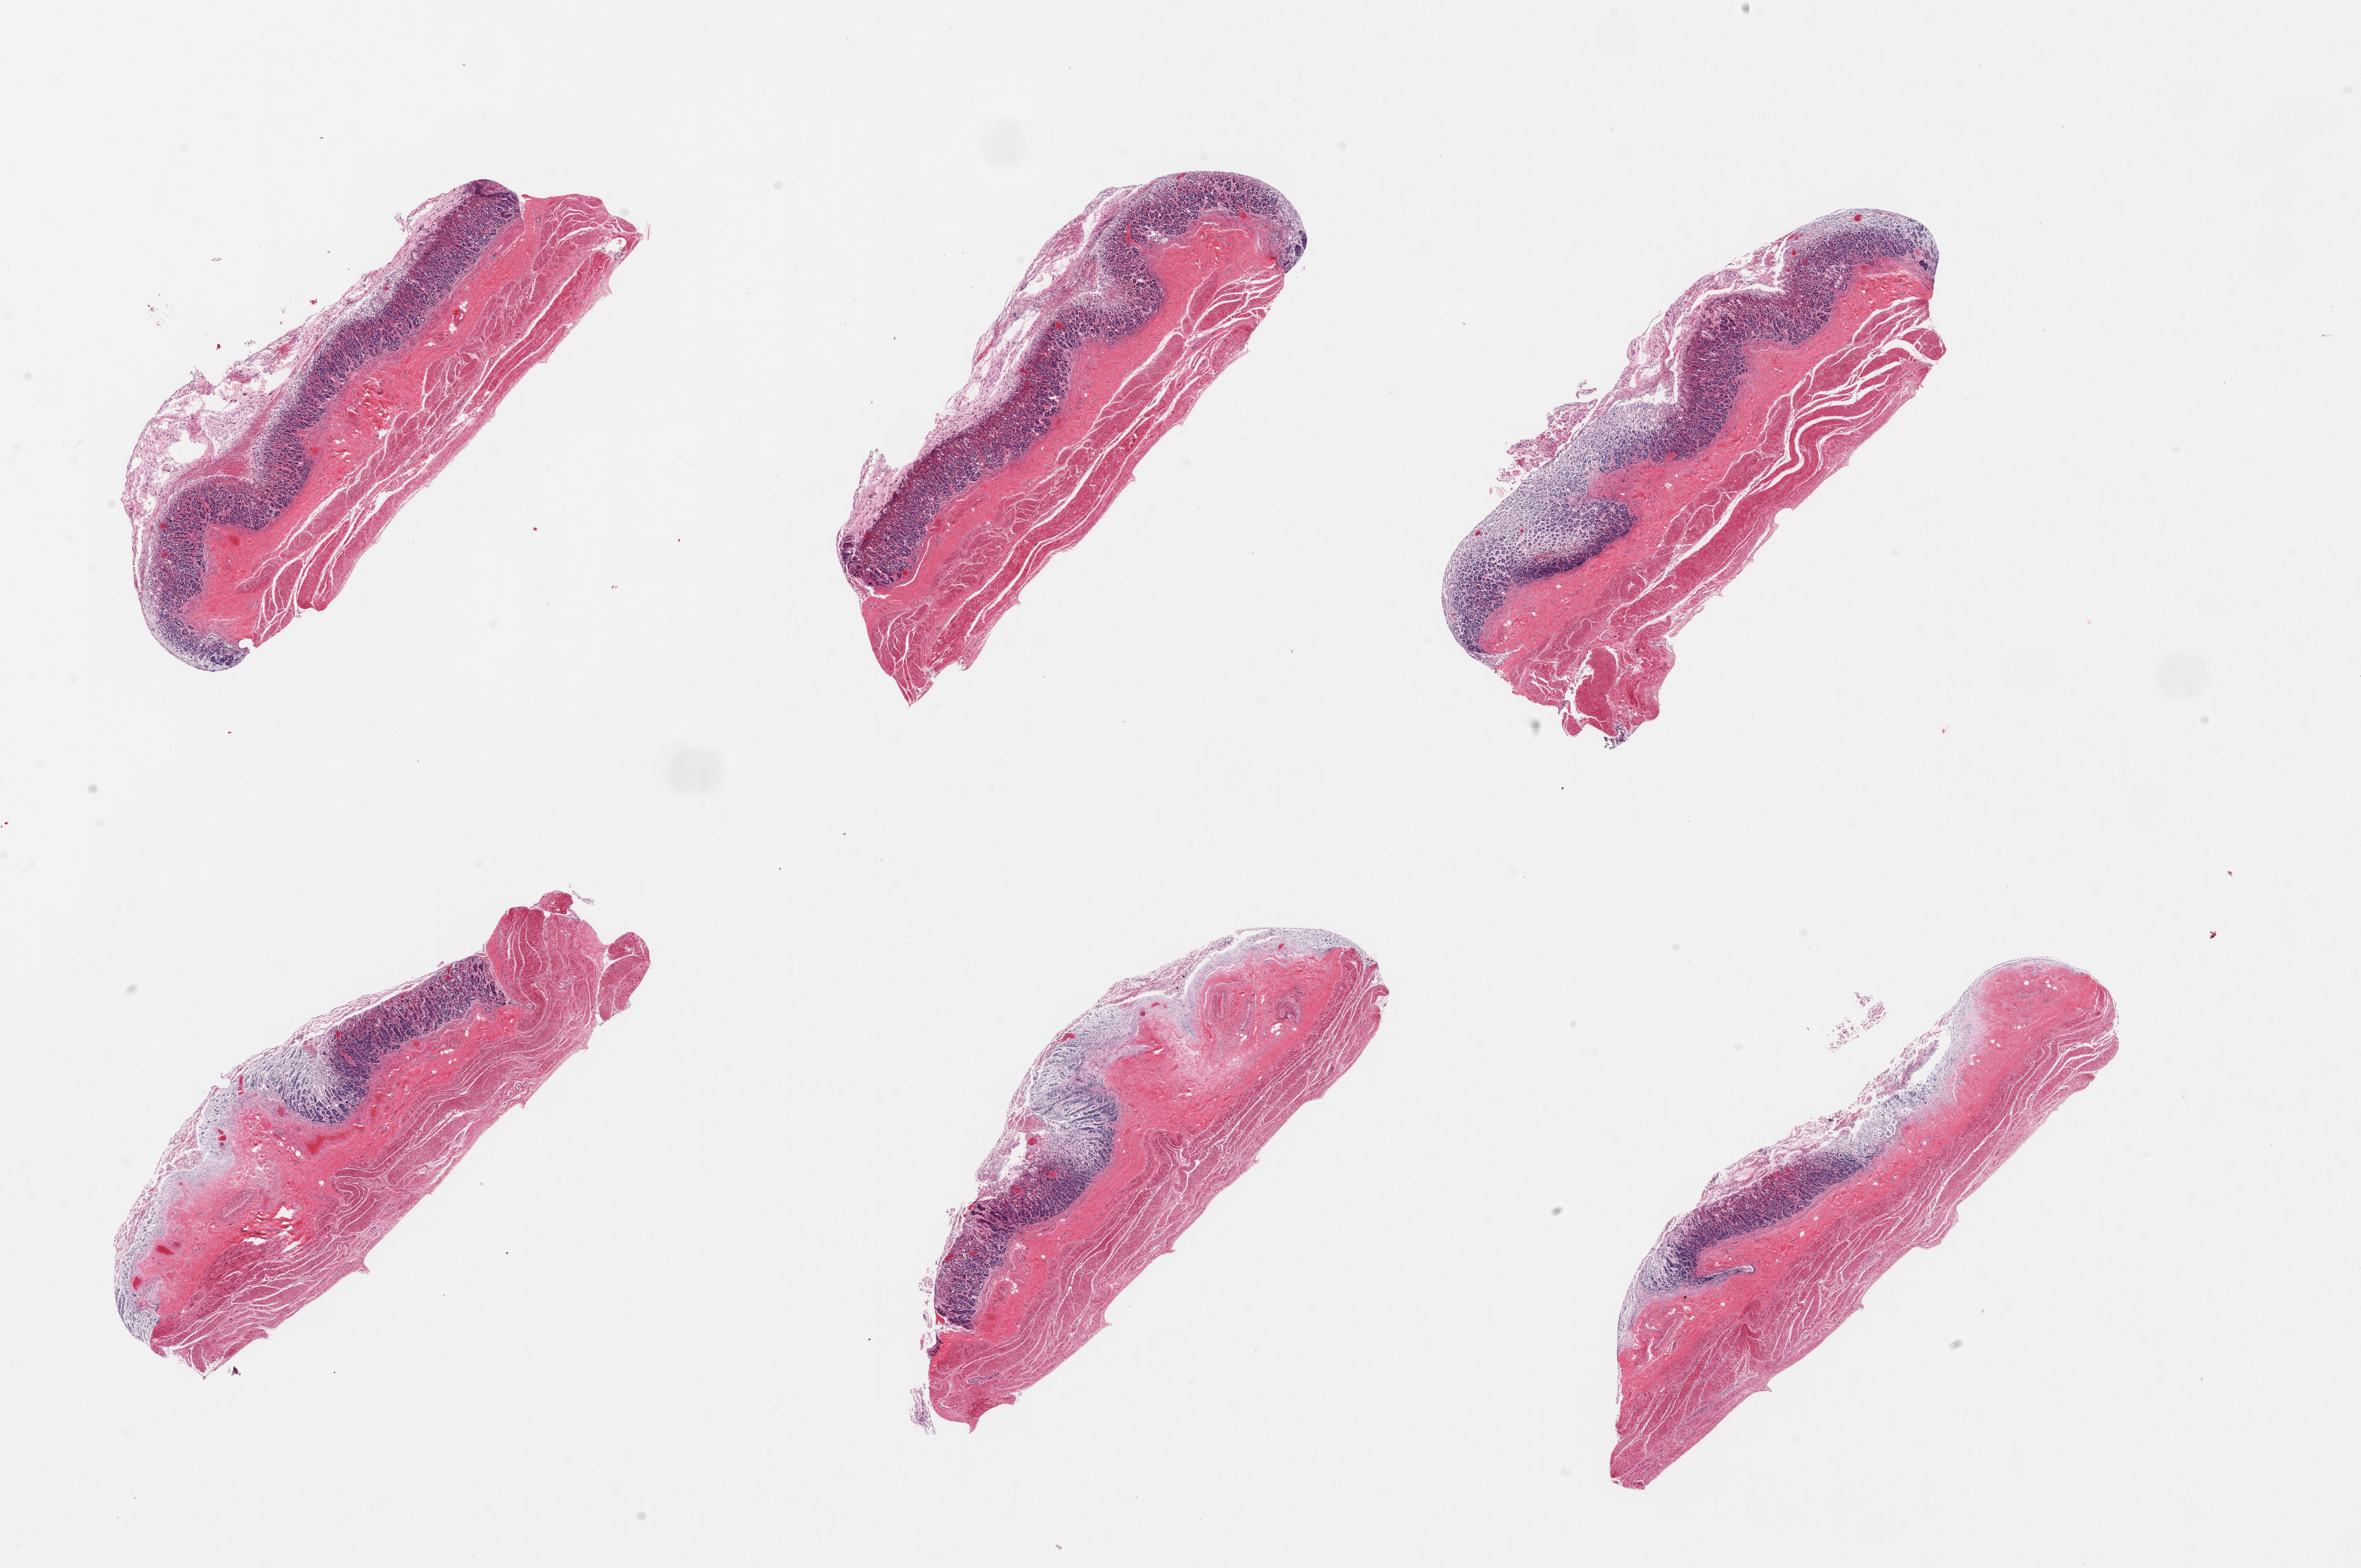
Digitized haematoxylin and eosin-stained section, a low-resolution overview of the entire scanned area, about 26.6 x 17.7 mm (from a 20x scan), PAXgene-fixed paraffin-embedded (PFPE) section, target tissue: stomach, donor tissue sample. Donor: female.
* reviewer comment on this tissue sample: 6 pieces, mucosa up to ~40 % thickness, moderate-advanced autolysis